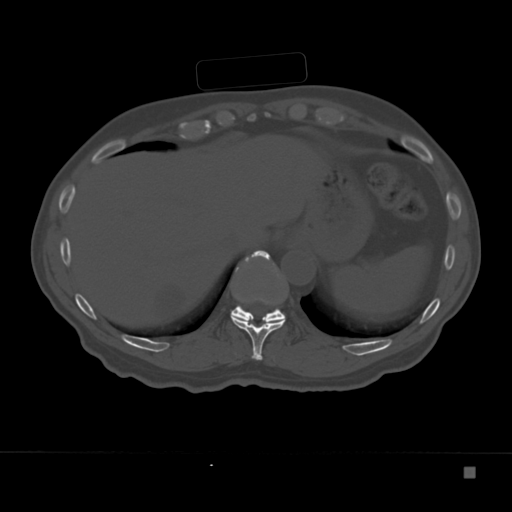
CT including the spine, one axial slice; slice 164 of 332 in the series (ordered by position); reconstruction kernel Br40s; bone window (W 1800 / L 400 HU); 1.5 mm slice thickness; 512 × 512 image matrix. Patient: male, 72 years. From the clinical record (not read from this slice): primary cancer: skeletal.
Outlined on this slice (semi-automatically segmented with operator editing):
- T10 vertebra: bounding box <231,251,285,360> (left, top, right, bottom; pixels)
- T11 vertebra: <231,250,285,323>